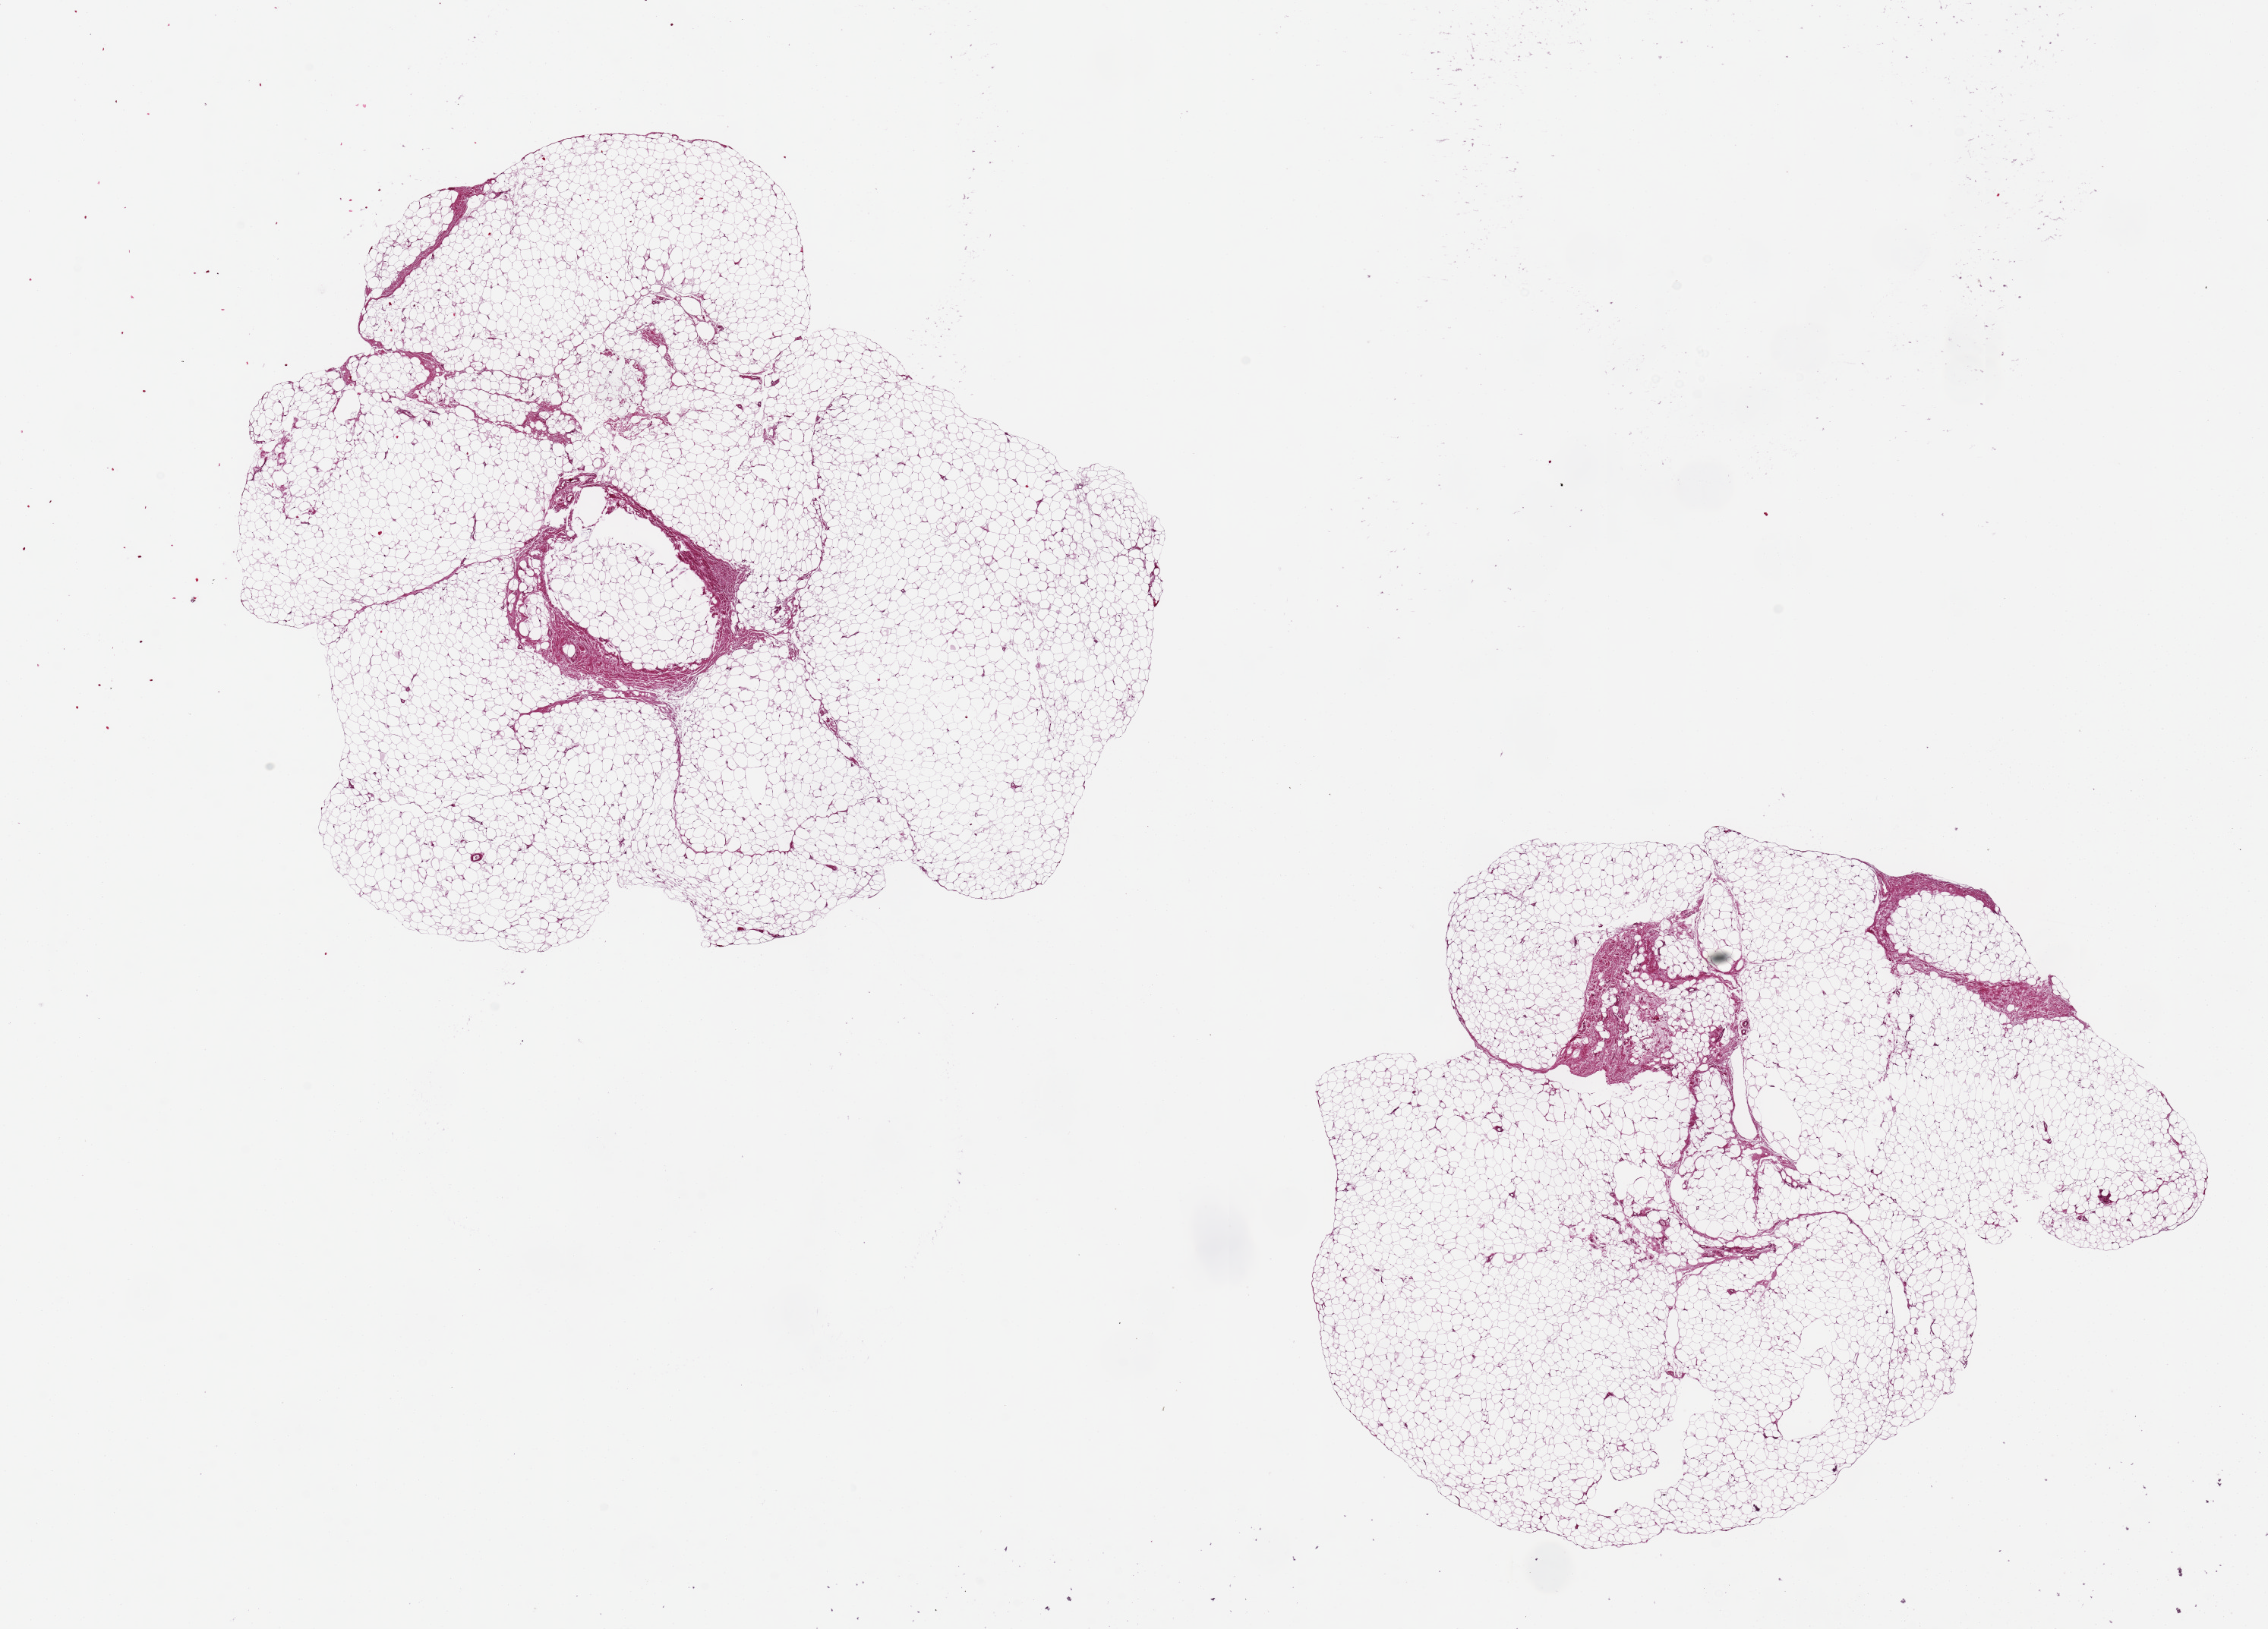
Digitized hematoxylin and eosin (H&E)-stained section, brightfield, shown as a low-resolution overview of the whole scanned area (about 23.6 x 17.0 mm); PAXgene-fixed paraffin-embedded (PFPE) section; target tissue: adipose tissue; donor tissue sample. Donor sex: female.
- review note (as recorded): 2 aliquots, ~9x8mm